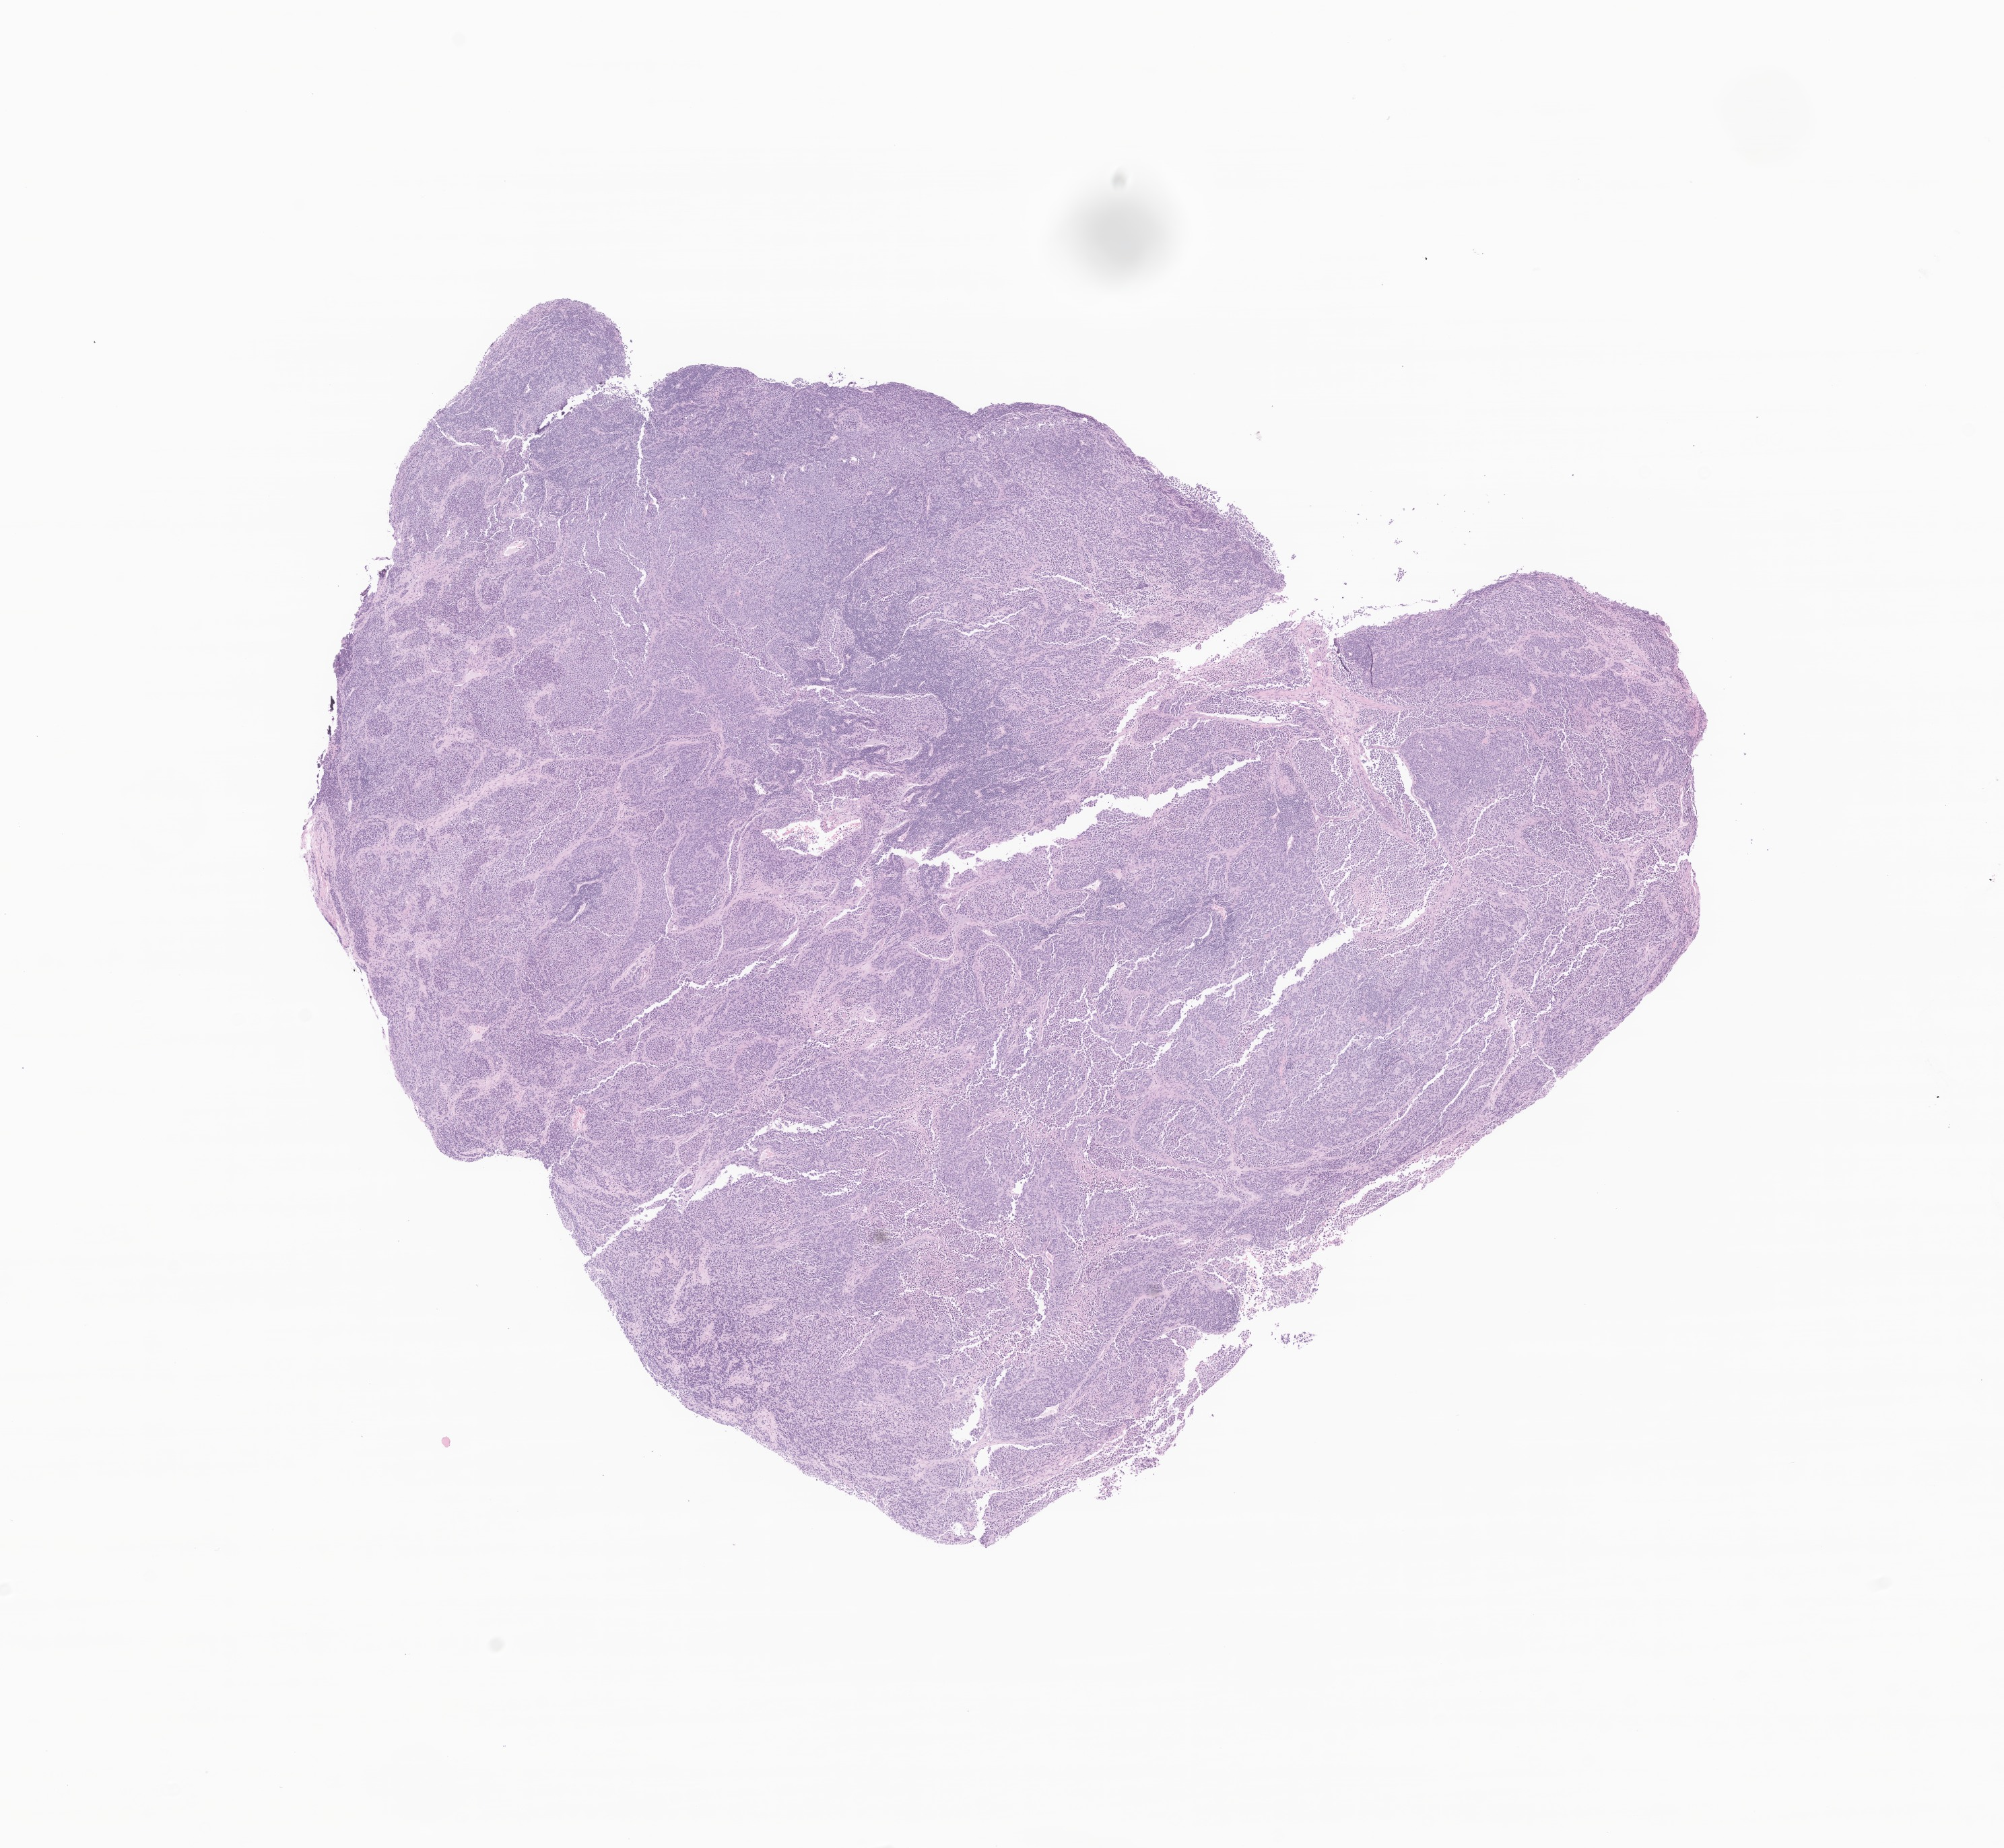
Whole-slide image, haematoxylin and eosin stain of tumor tissue from the head and neck lymph node, low-resolution overview of the scanned area, about 12.5 x 11.6 mm; FFPE section. Male patient, age 180 months.
* tissue or organ of origin (case record): lymph nodes of head, face and neck
* recorded diagnosis: Rhabdomyosarcoma, NOS